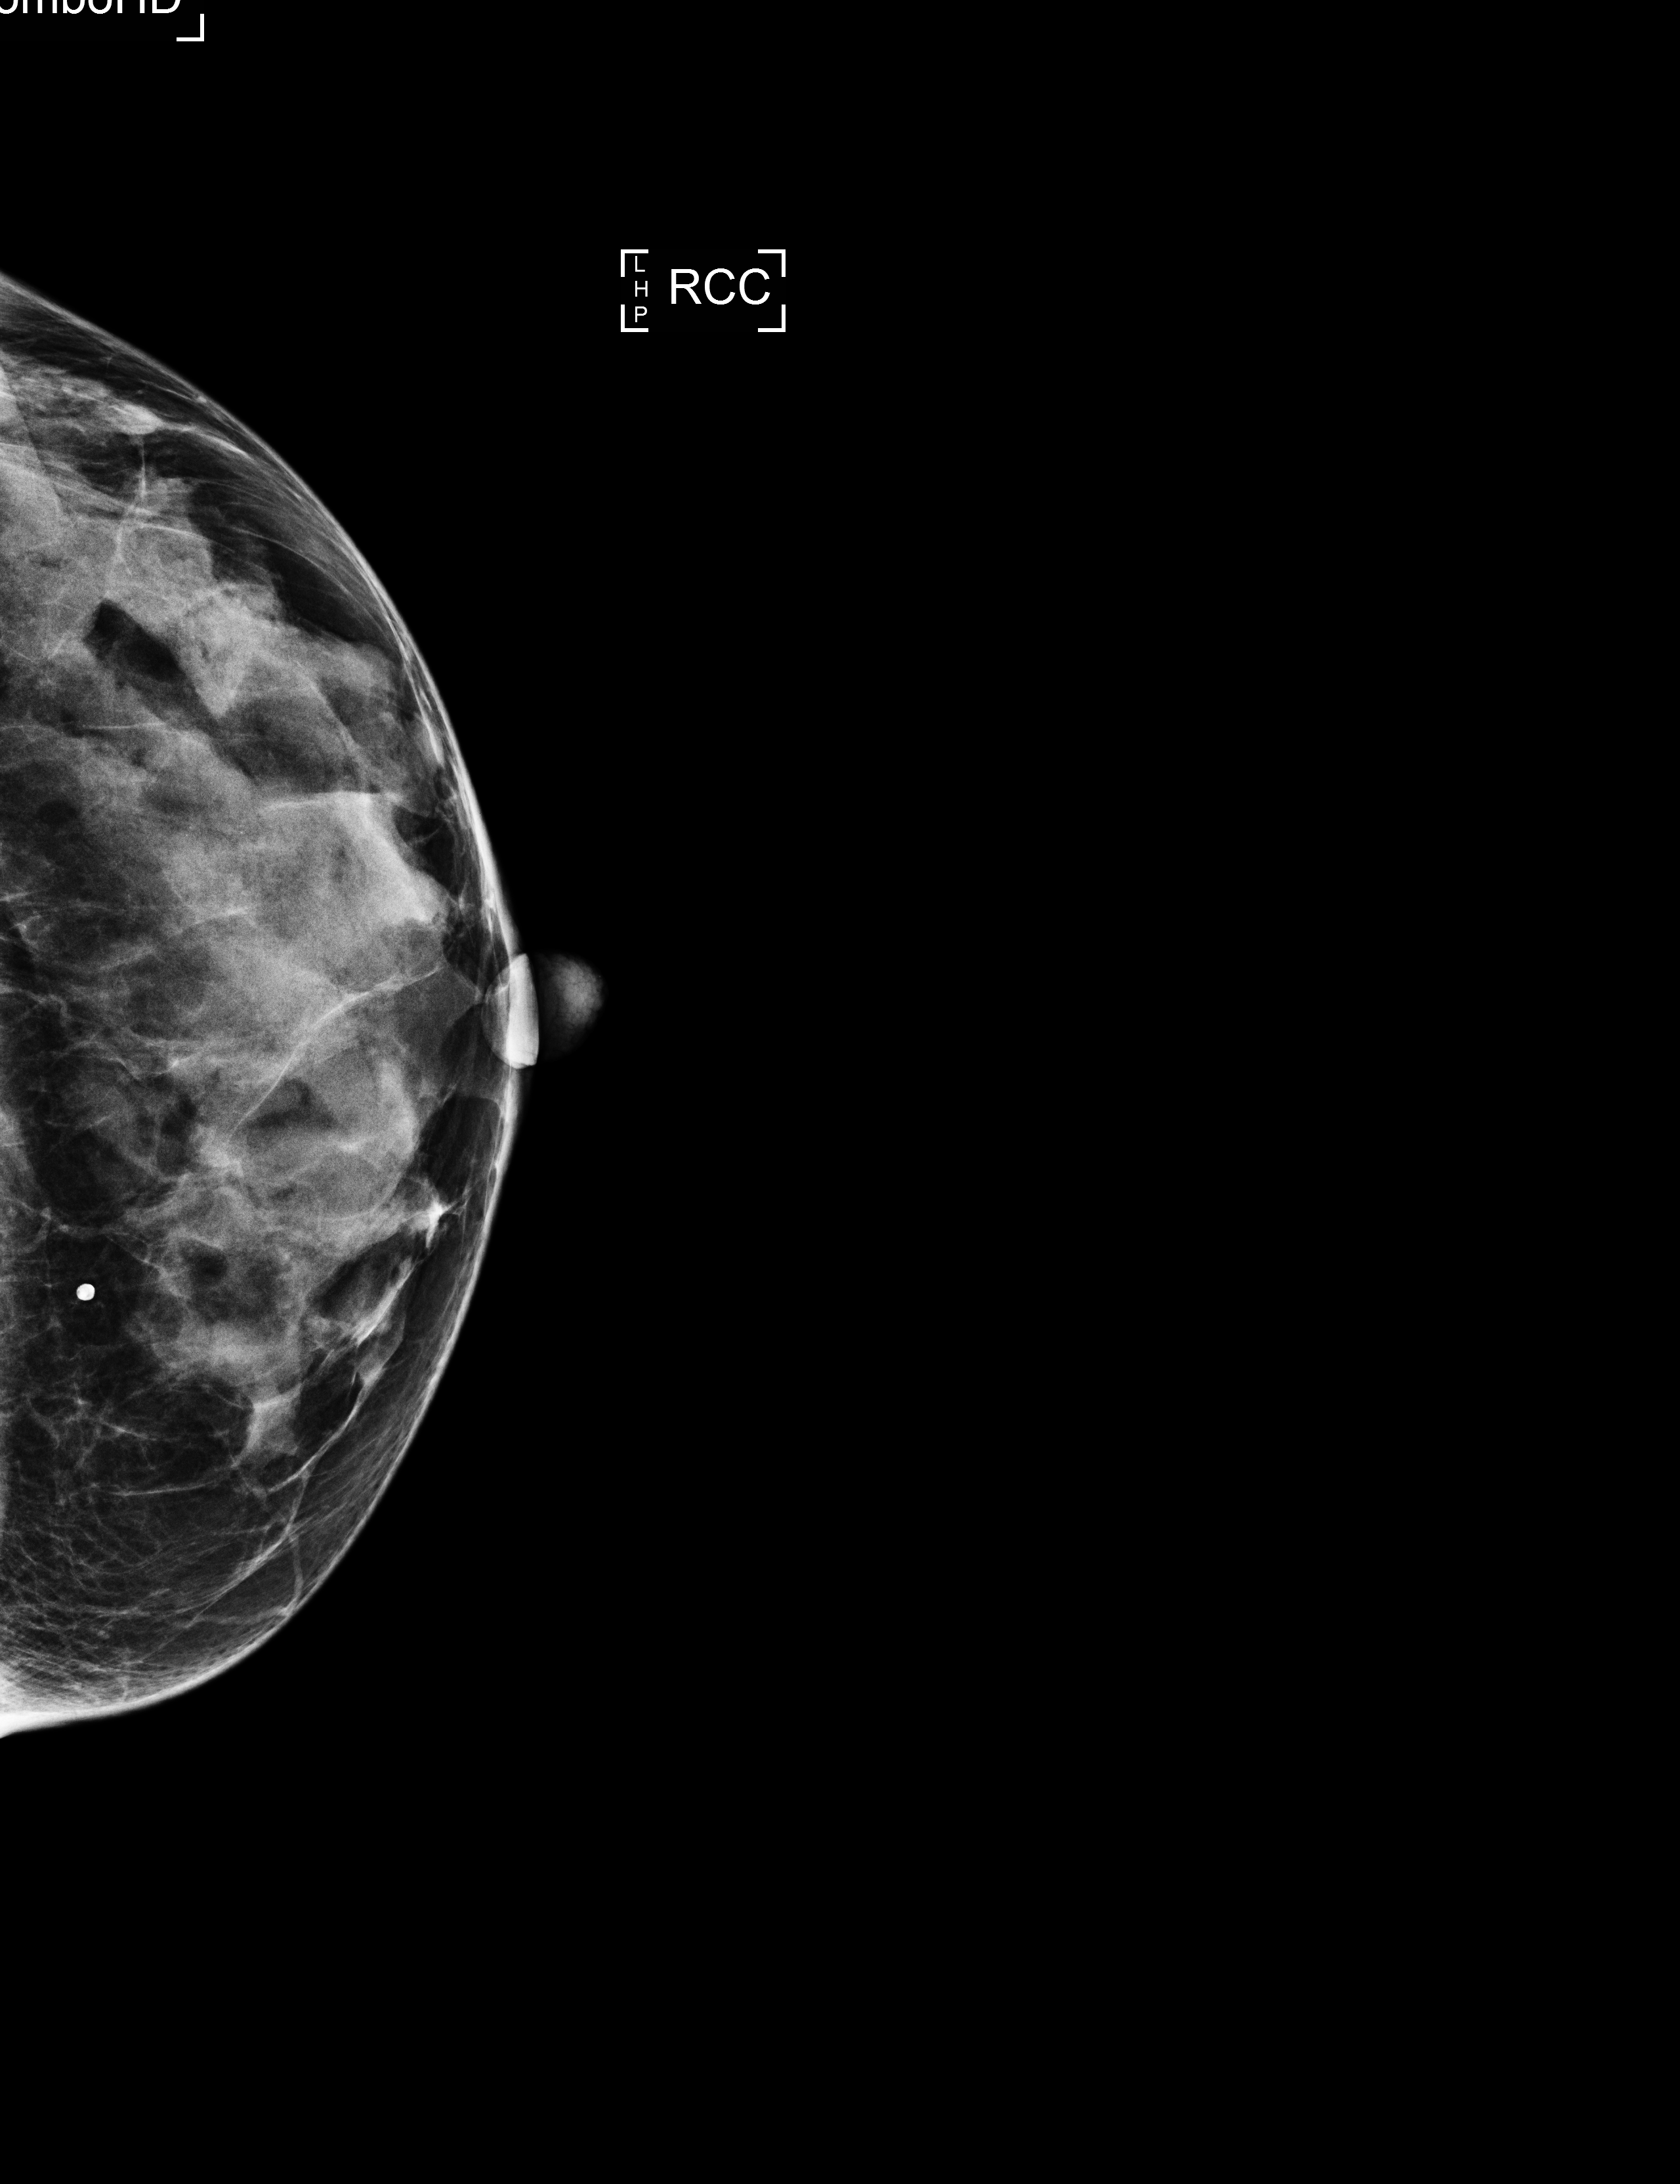
Annual screening mammography examination; system: Selenia Dimensions. Female patient, age 54 years.
Image type: full-field digital mammogram. Breast: right. Projection: CC view.